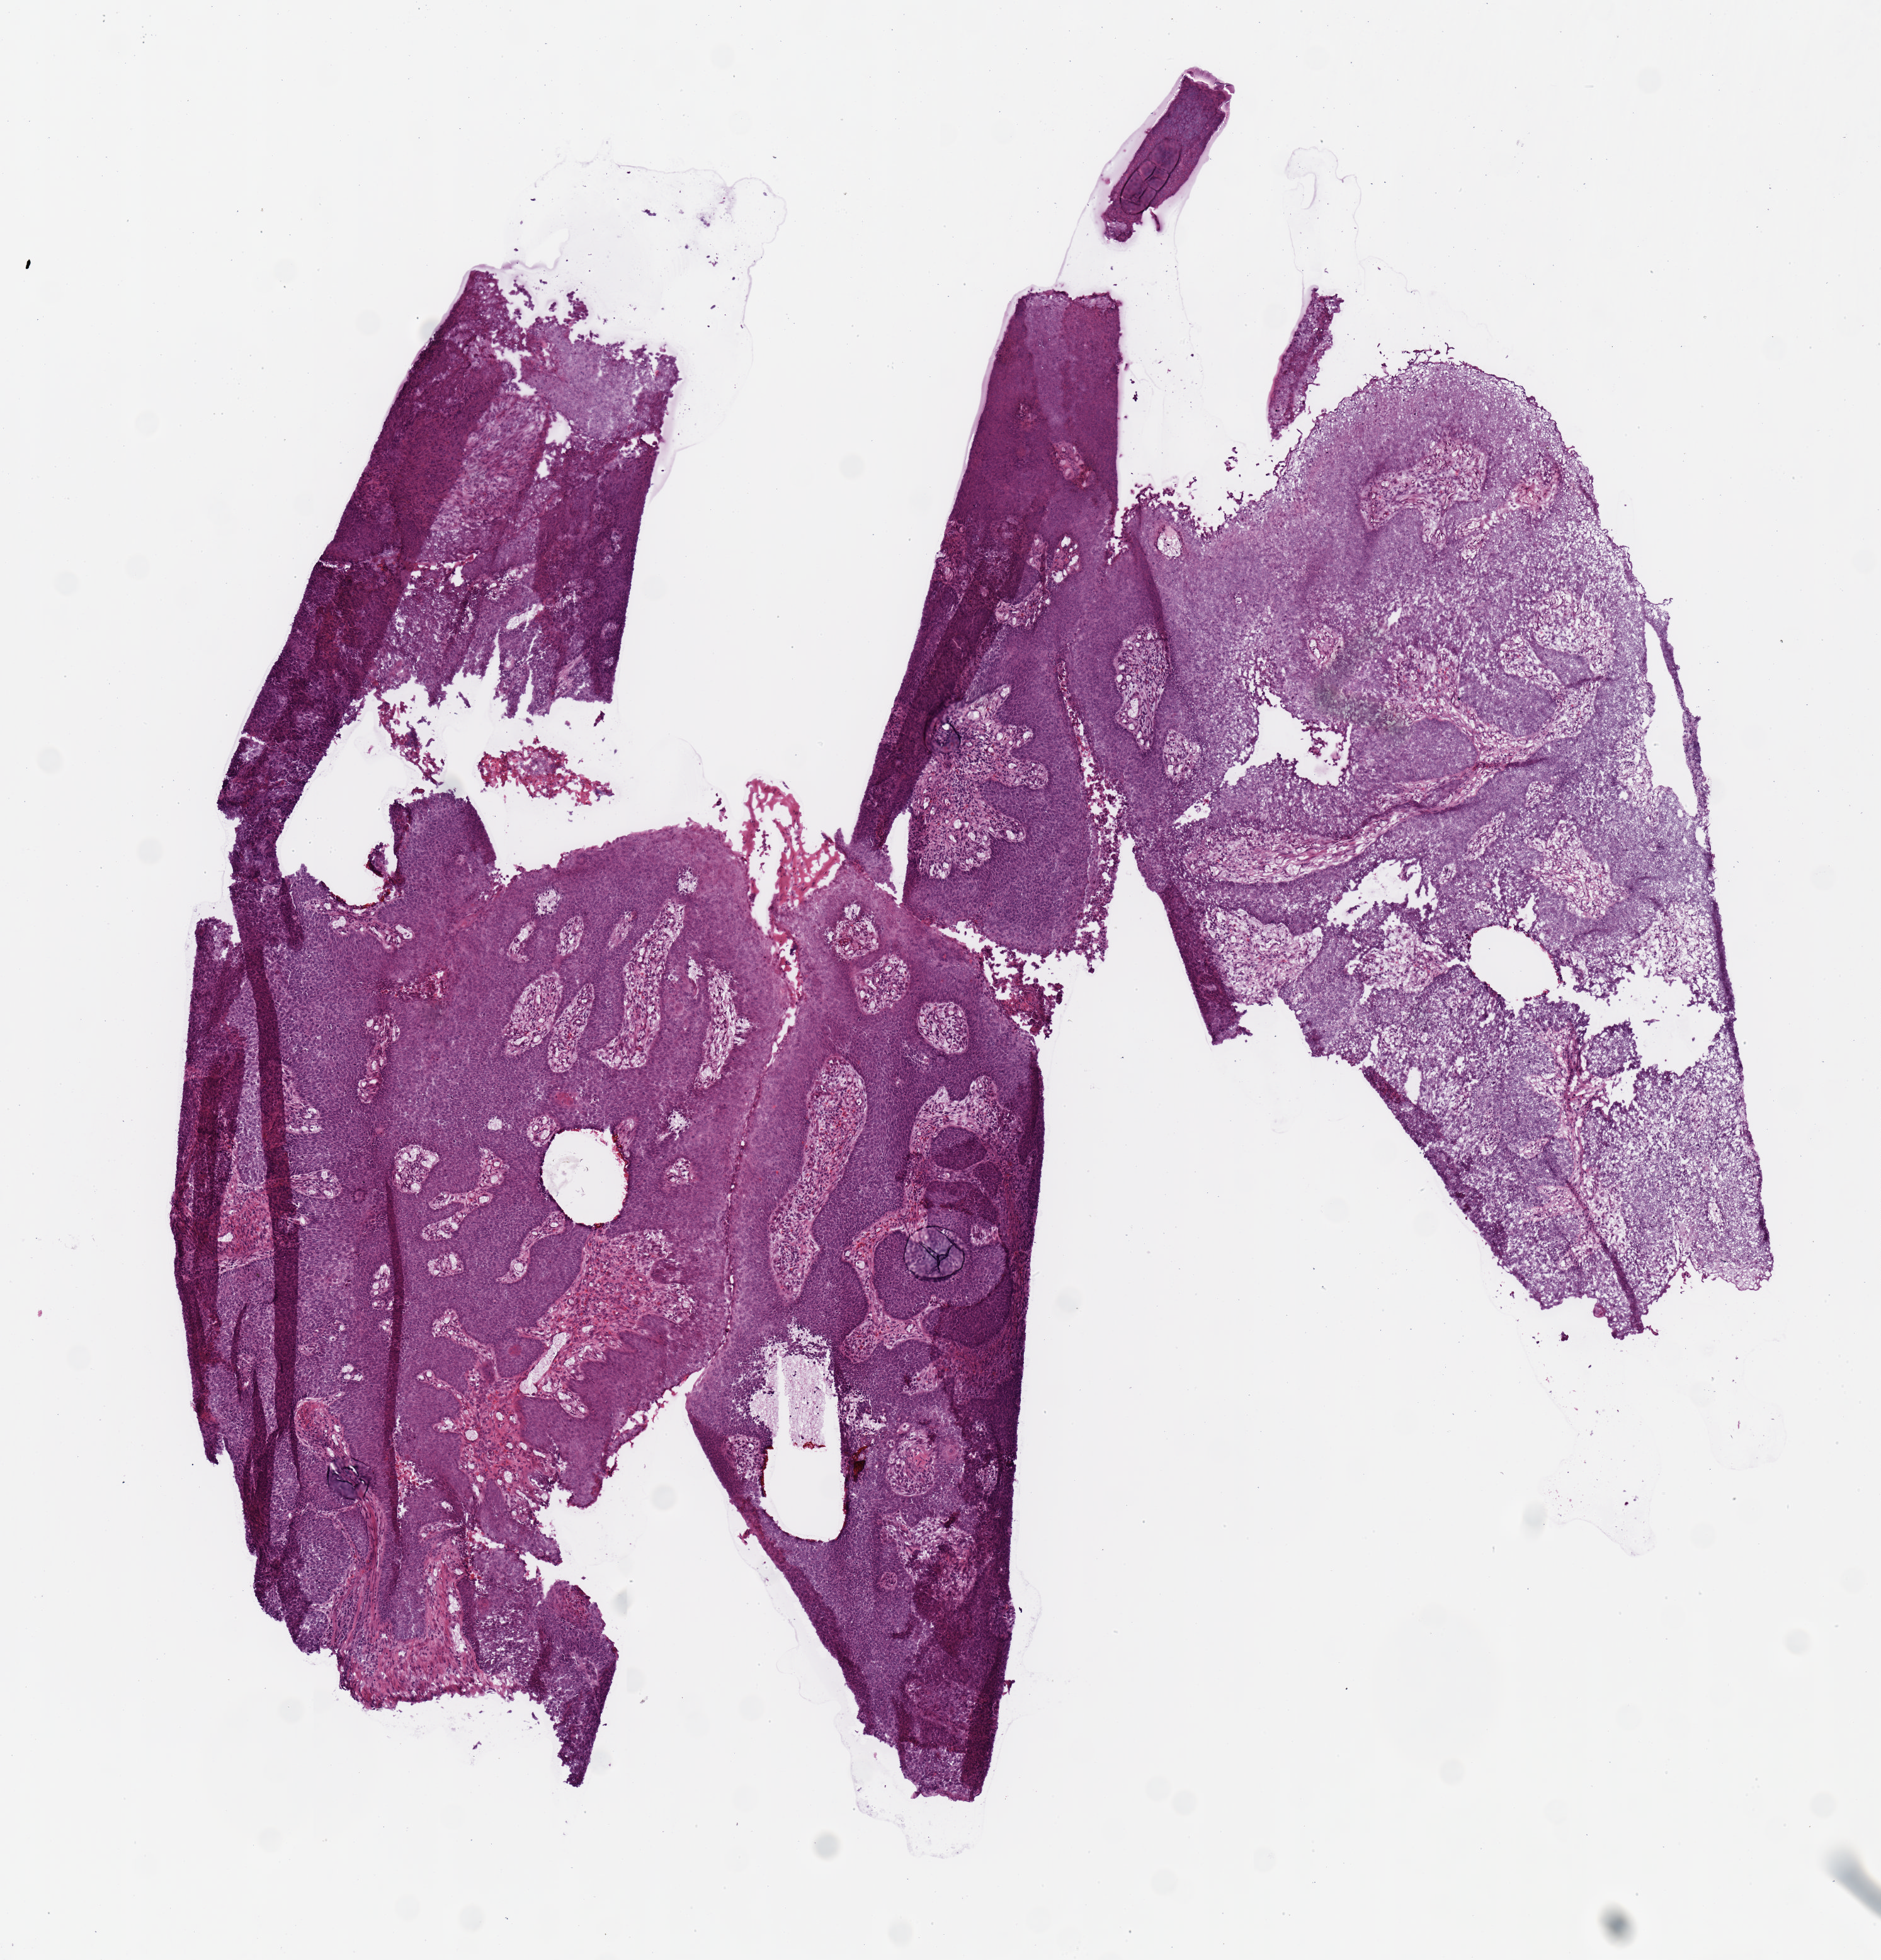
Whole-slide histology image, Hematoxylin and eosin (H&E) stained — low-resolution overview of the scanned area, about 5.9 x 6.2 mm (from a 20x scan). Frozen section from the top of the tissue portion. Primary tumour sample from the cervix. Female, age 43 years at initial diagnosis. Histologic grade: G2 (moderately differentiated). Slide review estimates, as recorded: tumour cells 85%, tumour nuclei 75%, normal cells 0%, stromal cells 15%, necrosis 0%. Infiltration values recorded for this section: lymphocyte infiltration 0%, monocyte infiltration 0%, neutrophil infiltration 0%.
Diagnosis: Squamous cell carcinoma, NOS (cervix uteri). FIGO stage: IIA2.